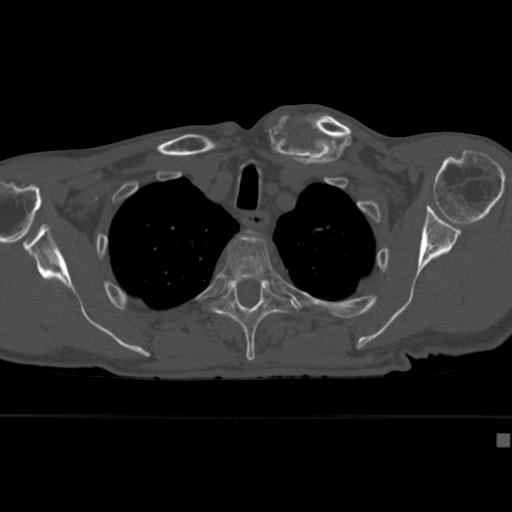
CT including the spine, one axial slice. Bone window (W 1800 / L 400 HU). 512 × 512 image matrix. Patient: male, 64 years. From the clinical record (not read from this slice): primary cancer: uterus.
Outlined on this slice (semi-automatic segmentation, software-assisted and operator-edited):
- T2 vertebra: bounding box <246,230,253,234> (left, top, right, bottom; pixels)
- T3 vertebra: <221,234,275,281>
- T4 vertebra: <209,280,299,362>